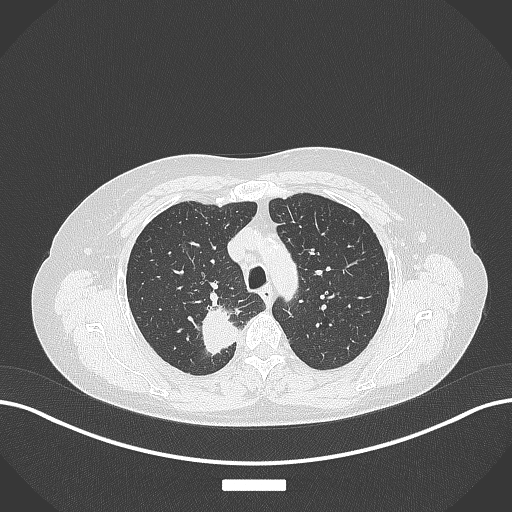
Chest CT, one axial slice; slice 295 of 357 in the series (ordered by position); reconstruction kernel B70f; 120 kVp; lung window (W 1500 / L -600 HU); 1 mm slice thickness; 512 × 512 image matrix. Female patient, age 62 years. Case-level facts recorded for this patient, not image findings: clinical TNM (as recorded): T1c N1 M0.
Outlined on this slice (rectangle marked by the reading radiologist):
- lung tumour (recorded histology: squamous cell carcinoma): bounding box <199,303,234,354> (left, top, right, bottom; pixels)